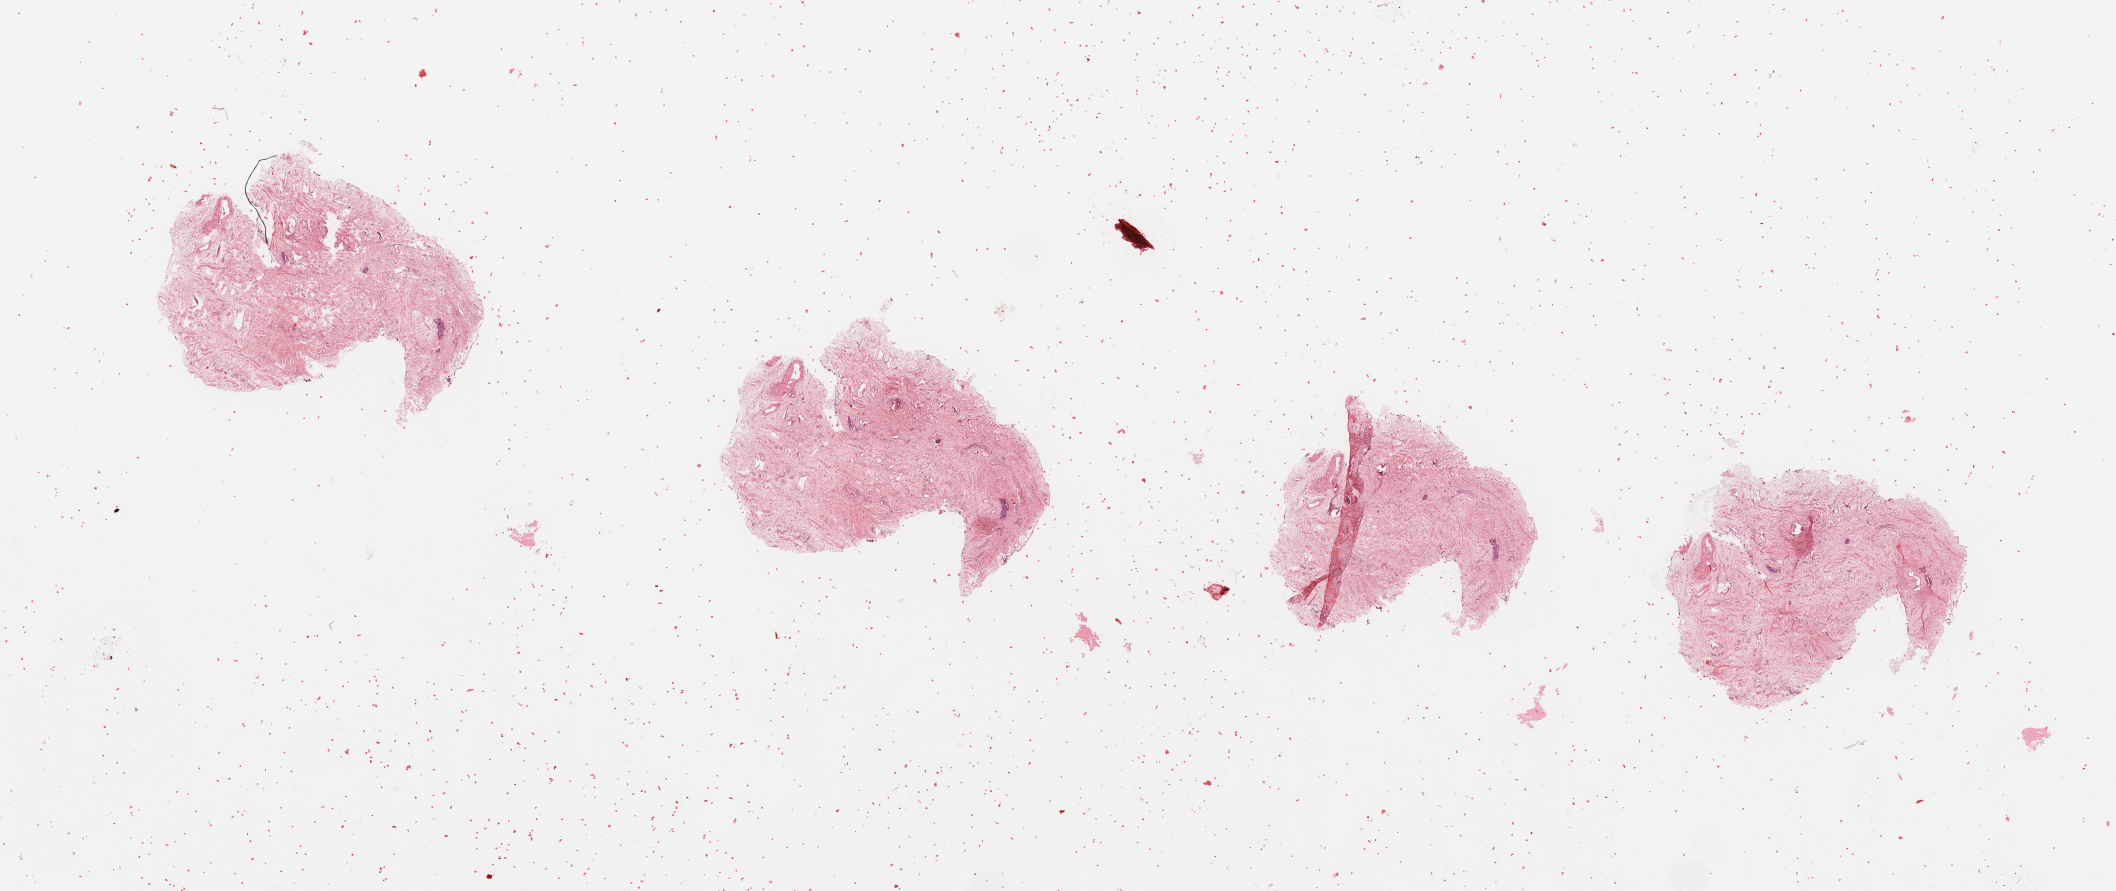
Digitized H&E-stained tissue section (whole slide), low-resolution overview of the scanned area, about 33.5 x 14.1 mm (from a 20x scan), normal (non-tumour) tissue sample, uterus. Female, 73 y/o.
* this section: normal (non-tumour) tissue from the same patient
* patient diagnosis: Endometrioid adenocarcinoma, NOS